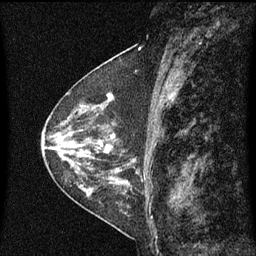
Breast MRI (dynamic contrast-enhanced), one sagittal slice. Slice 30 of 60 in the series (ordered by position). Dynamic contrast-enhanced series, image 2 of 3 at this slice position (ordered by acquisition). 1.5 T. TE 4.2 ms, TR 8 ms. 2 mm slice thickness. 256 × 256 image matrix. Patient: female, 48 years.
Outlined on this slice (semi-automatic segmentation, software-assisted and operator-edited):
- analysis volume of interest (the breast-tissue region the enhancement analysis was run in; not a lesion): bounding box <103,74,144,139> (left, top, right, bottom; pixels)
- tumour enhancement mask (voxels above the 70 % enhancement threshold inside the analysis volume of interest): <107,94,114,139>